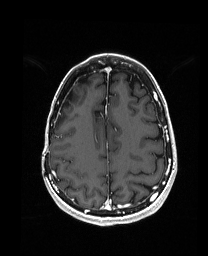
Brain MRI from a brain-tumour surgery series, one axial slice; position 55 of 192 along the scan axis; T1-weighted post-contrast; 1 mm slice thickness; 208 × 256 image matrix, field of view 203 × 250 mm. Case-level facts recorded for this patient, not image findings: histopathology: Metastatic Carcinoma from Breast primary; tumour location: Right Frontal.
Structures marked on this image (manually delineated by an expert):
- previous resection cavity: bounding box [x1, y1, x2, y2] px = [64, 90, 73, 106]